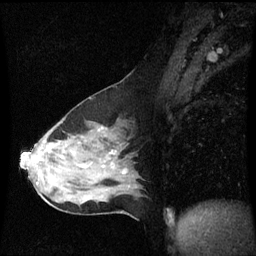
Breast MRI (dynamic contrast-enhanced), one sagittal slice. Slice 34 of 60 in the series (ordered by position). Dynamic contrast-enhanced series, image 2 of 3 at this slice position (ordered by acquisition). 1.5 T. TE 4.2 ms, TR 8.9 ms. 2 mm slice thickness. 256 × 256 image matrix, field of view 210 × 210 mm. Female patient, age 50 years. Case-level facts recorded for this patient, not image findings: setting: breast cancer imaged before/during neoadjuvant chemotherapy; receptor status: HR-positive, HER2-negative.
Annotated regions visible in this slice (semi-automatic segmentation, software-assisted and operator-edited):
- analysis volume of interest (the breast-tissue region the enhancement analysis was run in; not a lesion): bounding box (x1, y1, x2, y2) in pixels: (20, 98, 141, 210)
- tumour enhancement mask (voxels above the 70 % enhancement threshold inside the analysis volume of interest): (102, 128, 114, 154)